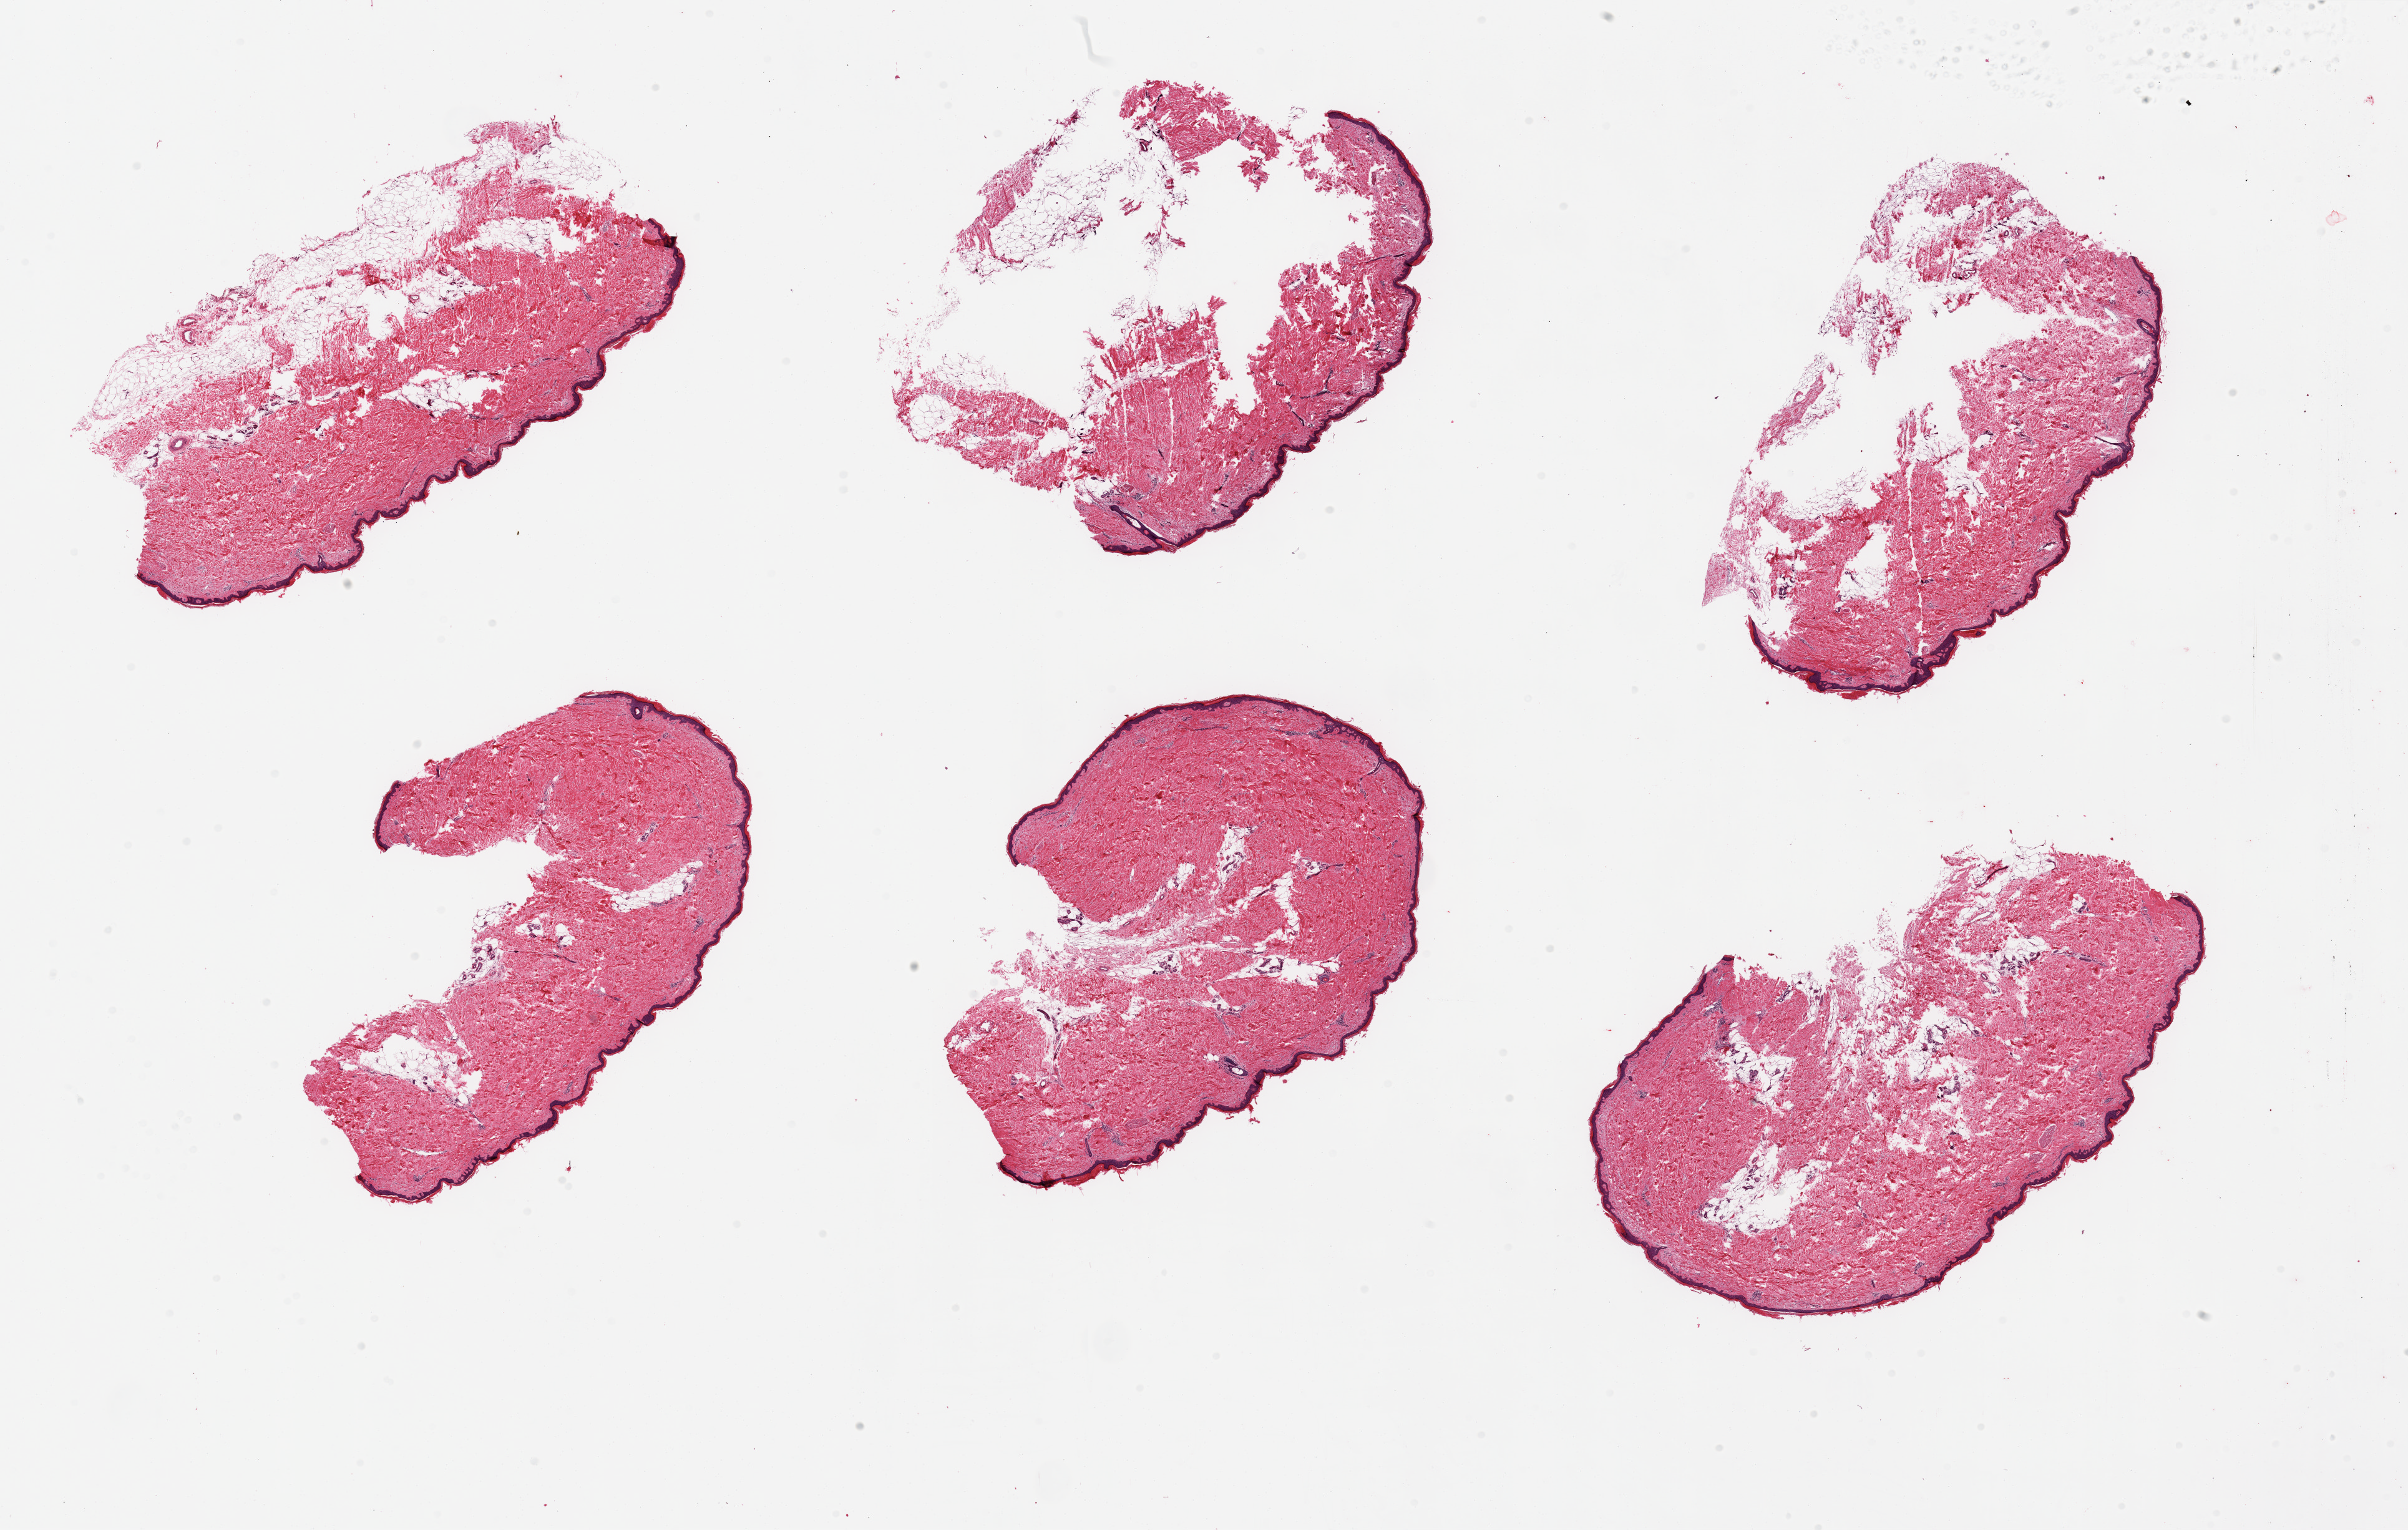
Whole-slide image, hematoxylin and eosin (H&E) stain, brightfield — a low-resolution overview of the entire scanned area, about 30.5 x 19.4 mm (acquisition: 20x scan); PAXgene-fixed, paraffin-embedded tissue; sampled site (target tissue): skin of lower leg; donor tissue sample. Female donor.
* reviewer comment on this tissue sample: 6 pieces; excessive subcutaneous fat and up to 20% dermal fat